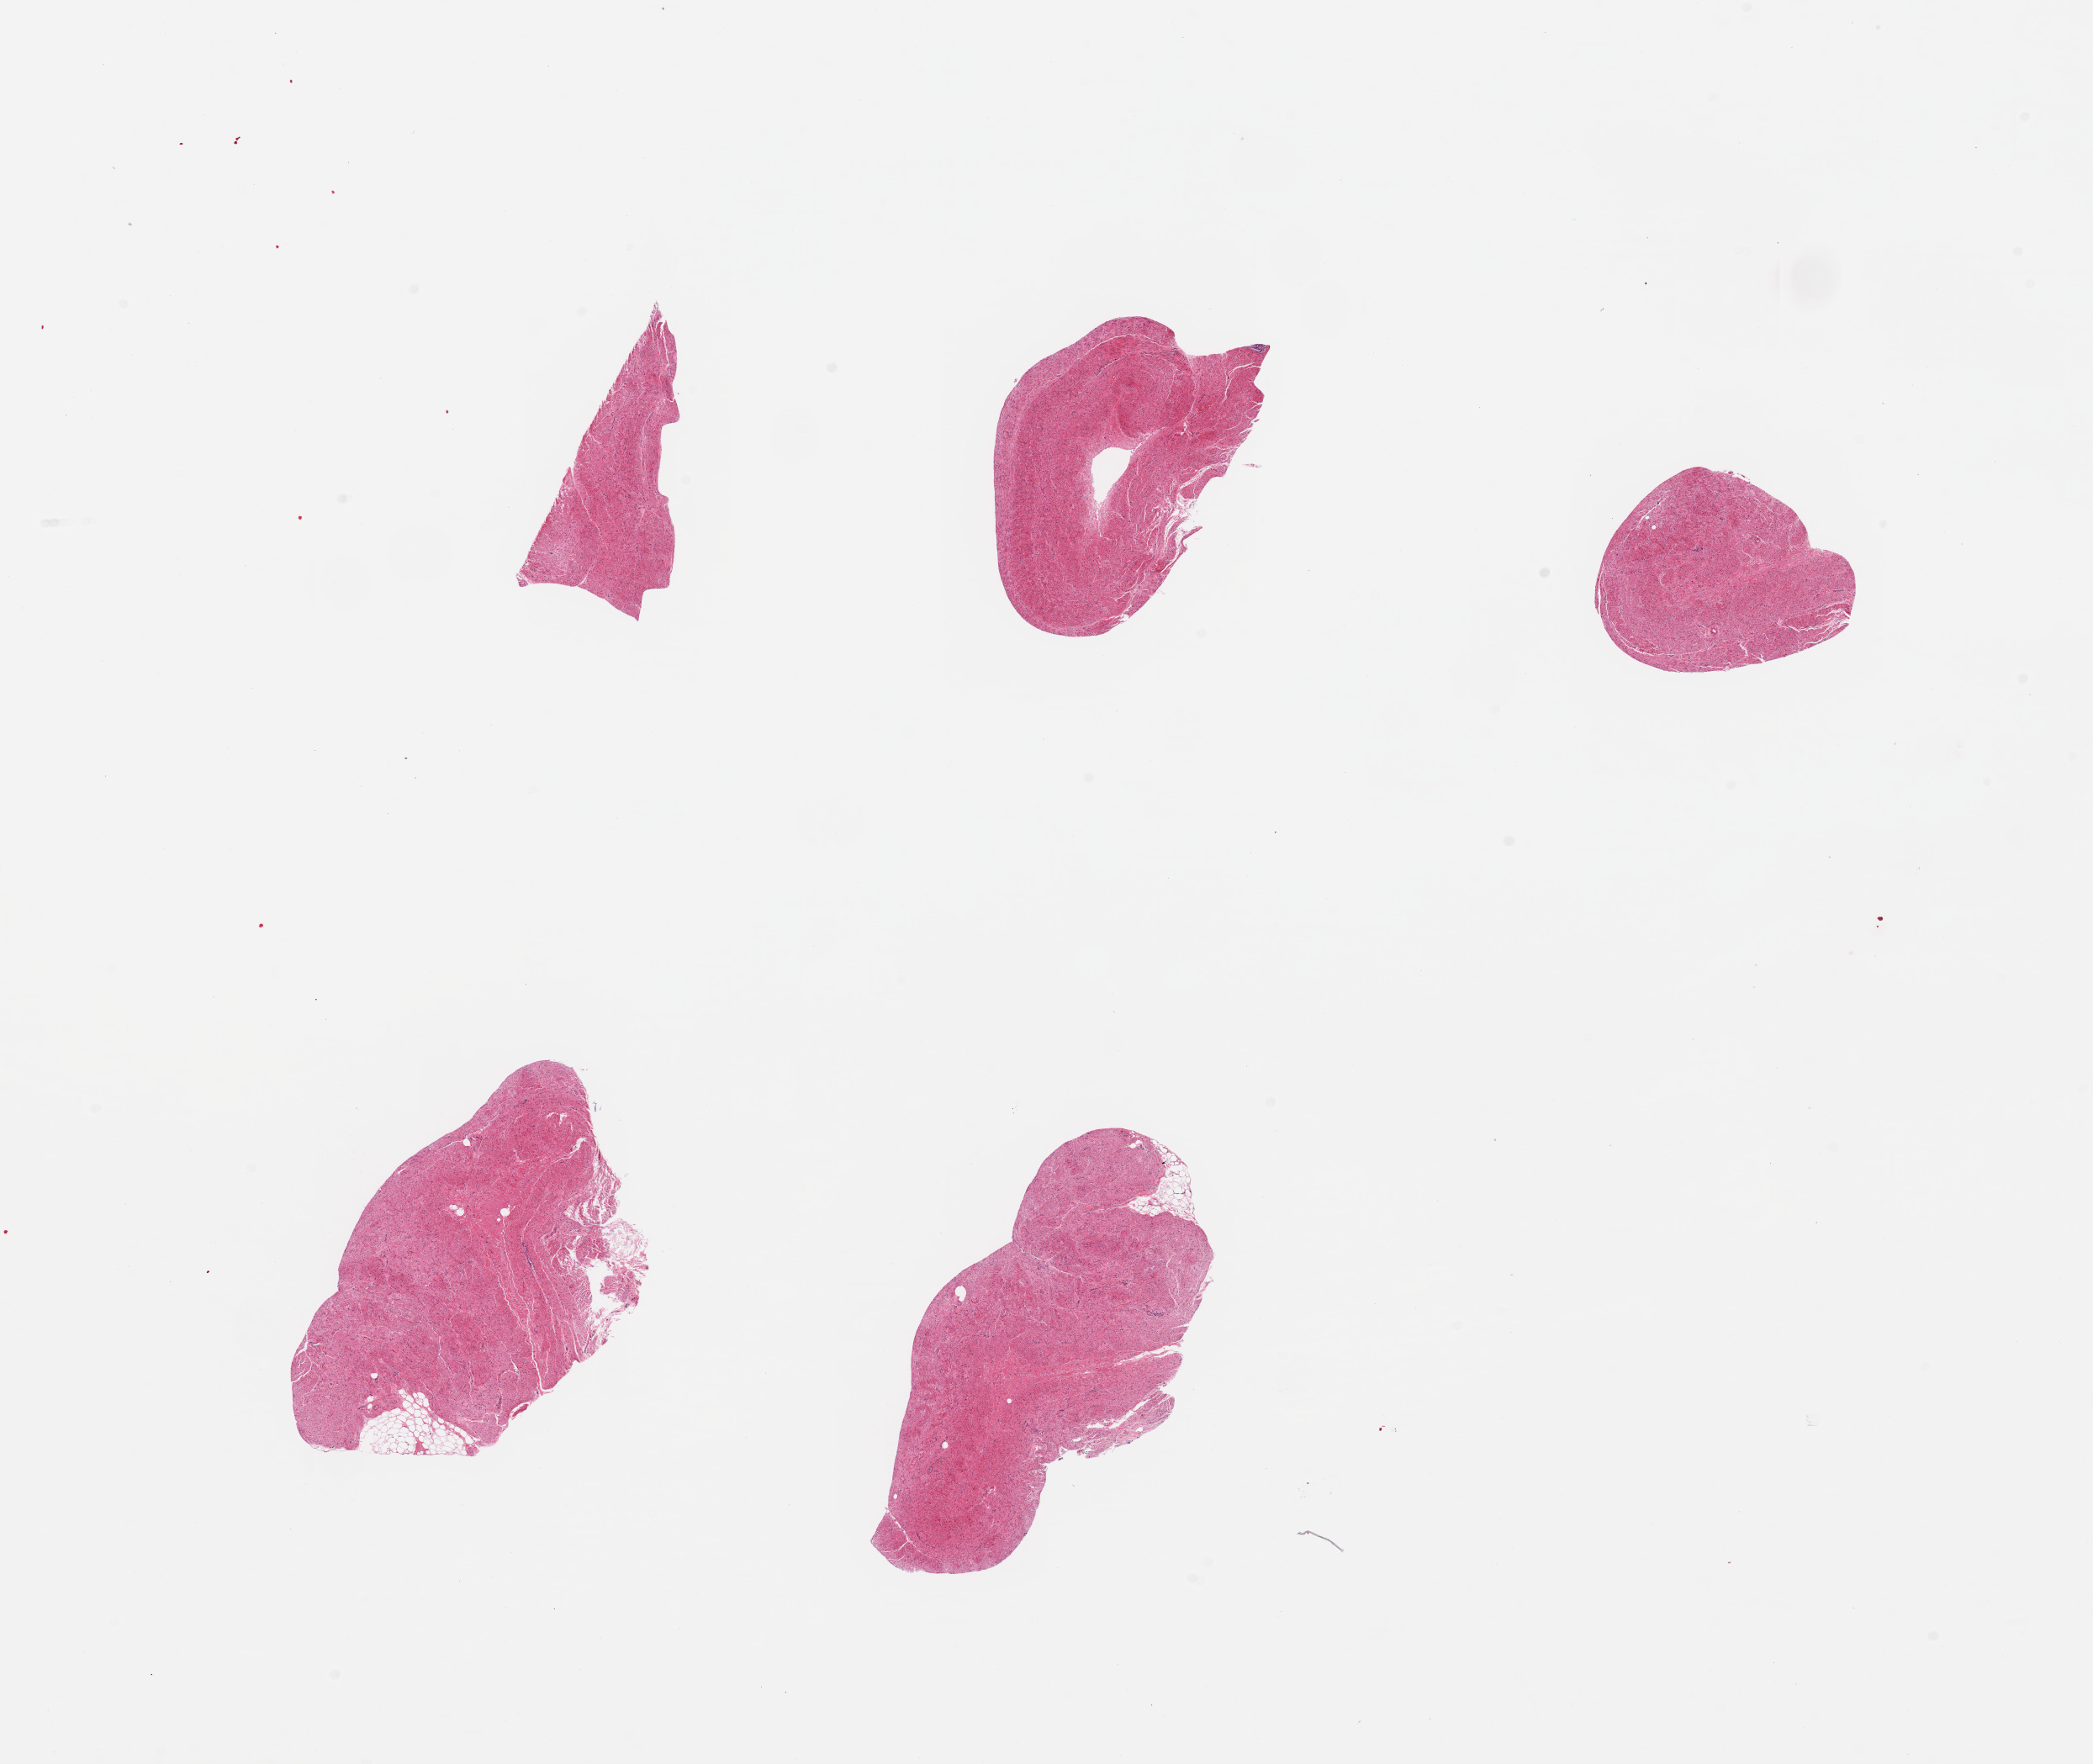
Digitized hematoxylin and eosin (H&E)-stained section, whole scanned area (about 19.7 x 16.6 mm, acquisition: 20x scan) shown as a low-resolution overview, PAXgene-fixed paraffin-embedded (PFPE) section, target tissue: stomach, tissue donor sample. Female donor.
Review note (as recorded): 5 pieces, muscularis only.